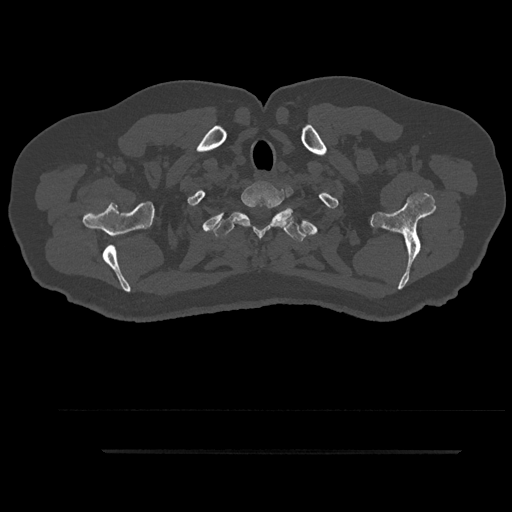
CT including the spine, one axial slice. Slice 782 of 797 in the series (ordered by position). Bone window (W 1800 / L 400 HU). 0.5 mm slice thickness. 512 × 512 image matrix, field of view 432 × 432 mm. Patient: male, 63 years. Case-level facts recorded for this patient, not image findings: primary cancer: renal.
Structures marked on this image (semi-automatically segmented with operator editing):
- T1 vertebra: bounding box (x1, y1, x2, y2) in pixels: (232, 185, 291, 238)
- T2 vertebra: (213, 206, 306, 242)